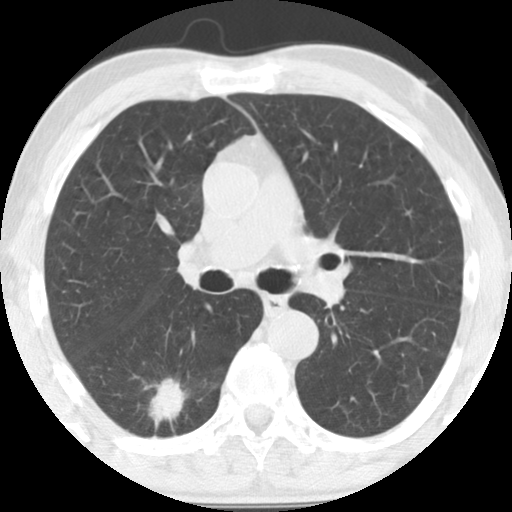
Low-dose screening chest CT, axial slice, baseline screening round, lung window (W 1500 / L -600 HU), 2.5 mm slice thickness, standard (soft-tissue) reconstruction kernel (STANDARD), 120 kVp. Male, age 64 years at enrolment. Current smoker at enrolment.
Expert-annotated lung lesion, bounding box <117,366,191,433> (left, top, right, bottom; pixels). The exam's reader record, not a measurement of the box and not confirmed to be the same lesion: non-calcified nodule or mass ≥4 mm, right lower lobe, 36 × 26 mm, spiculated (stellate) margins, soft tissue attenuation. Official screen result: positive, change unspecified: nodule(s) >= 4 mm or enlarging nodule(s), mass(es), or other non-specific abnormalities suspicious for lung cancer. Participant outcome: lung cancer diagnosed 20 days after this screen — adenocarcinoma, NOS, right lower lobe, moderately differentiated (G2), stage IA (AJCC 6th edition), 28 mm at pathology.